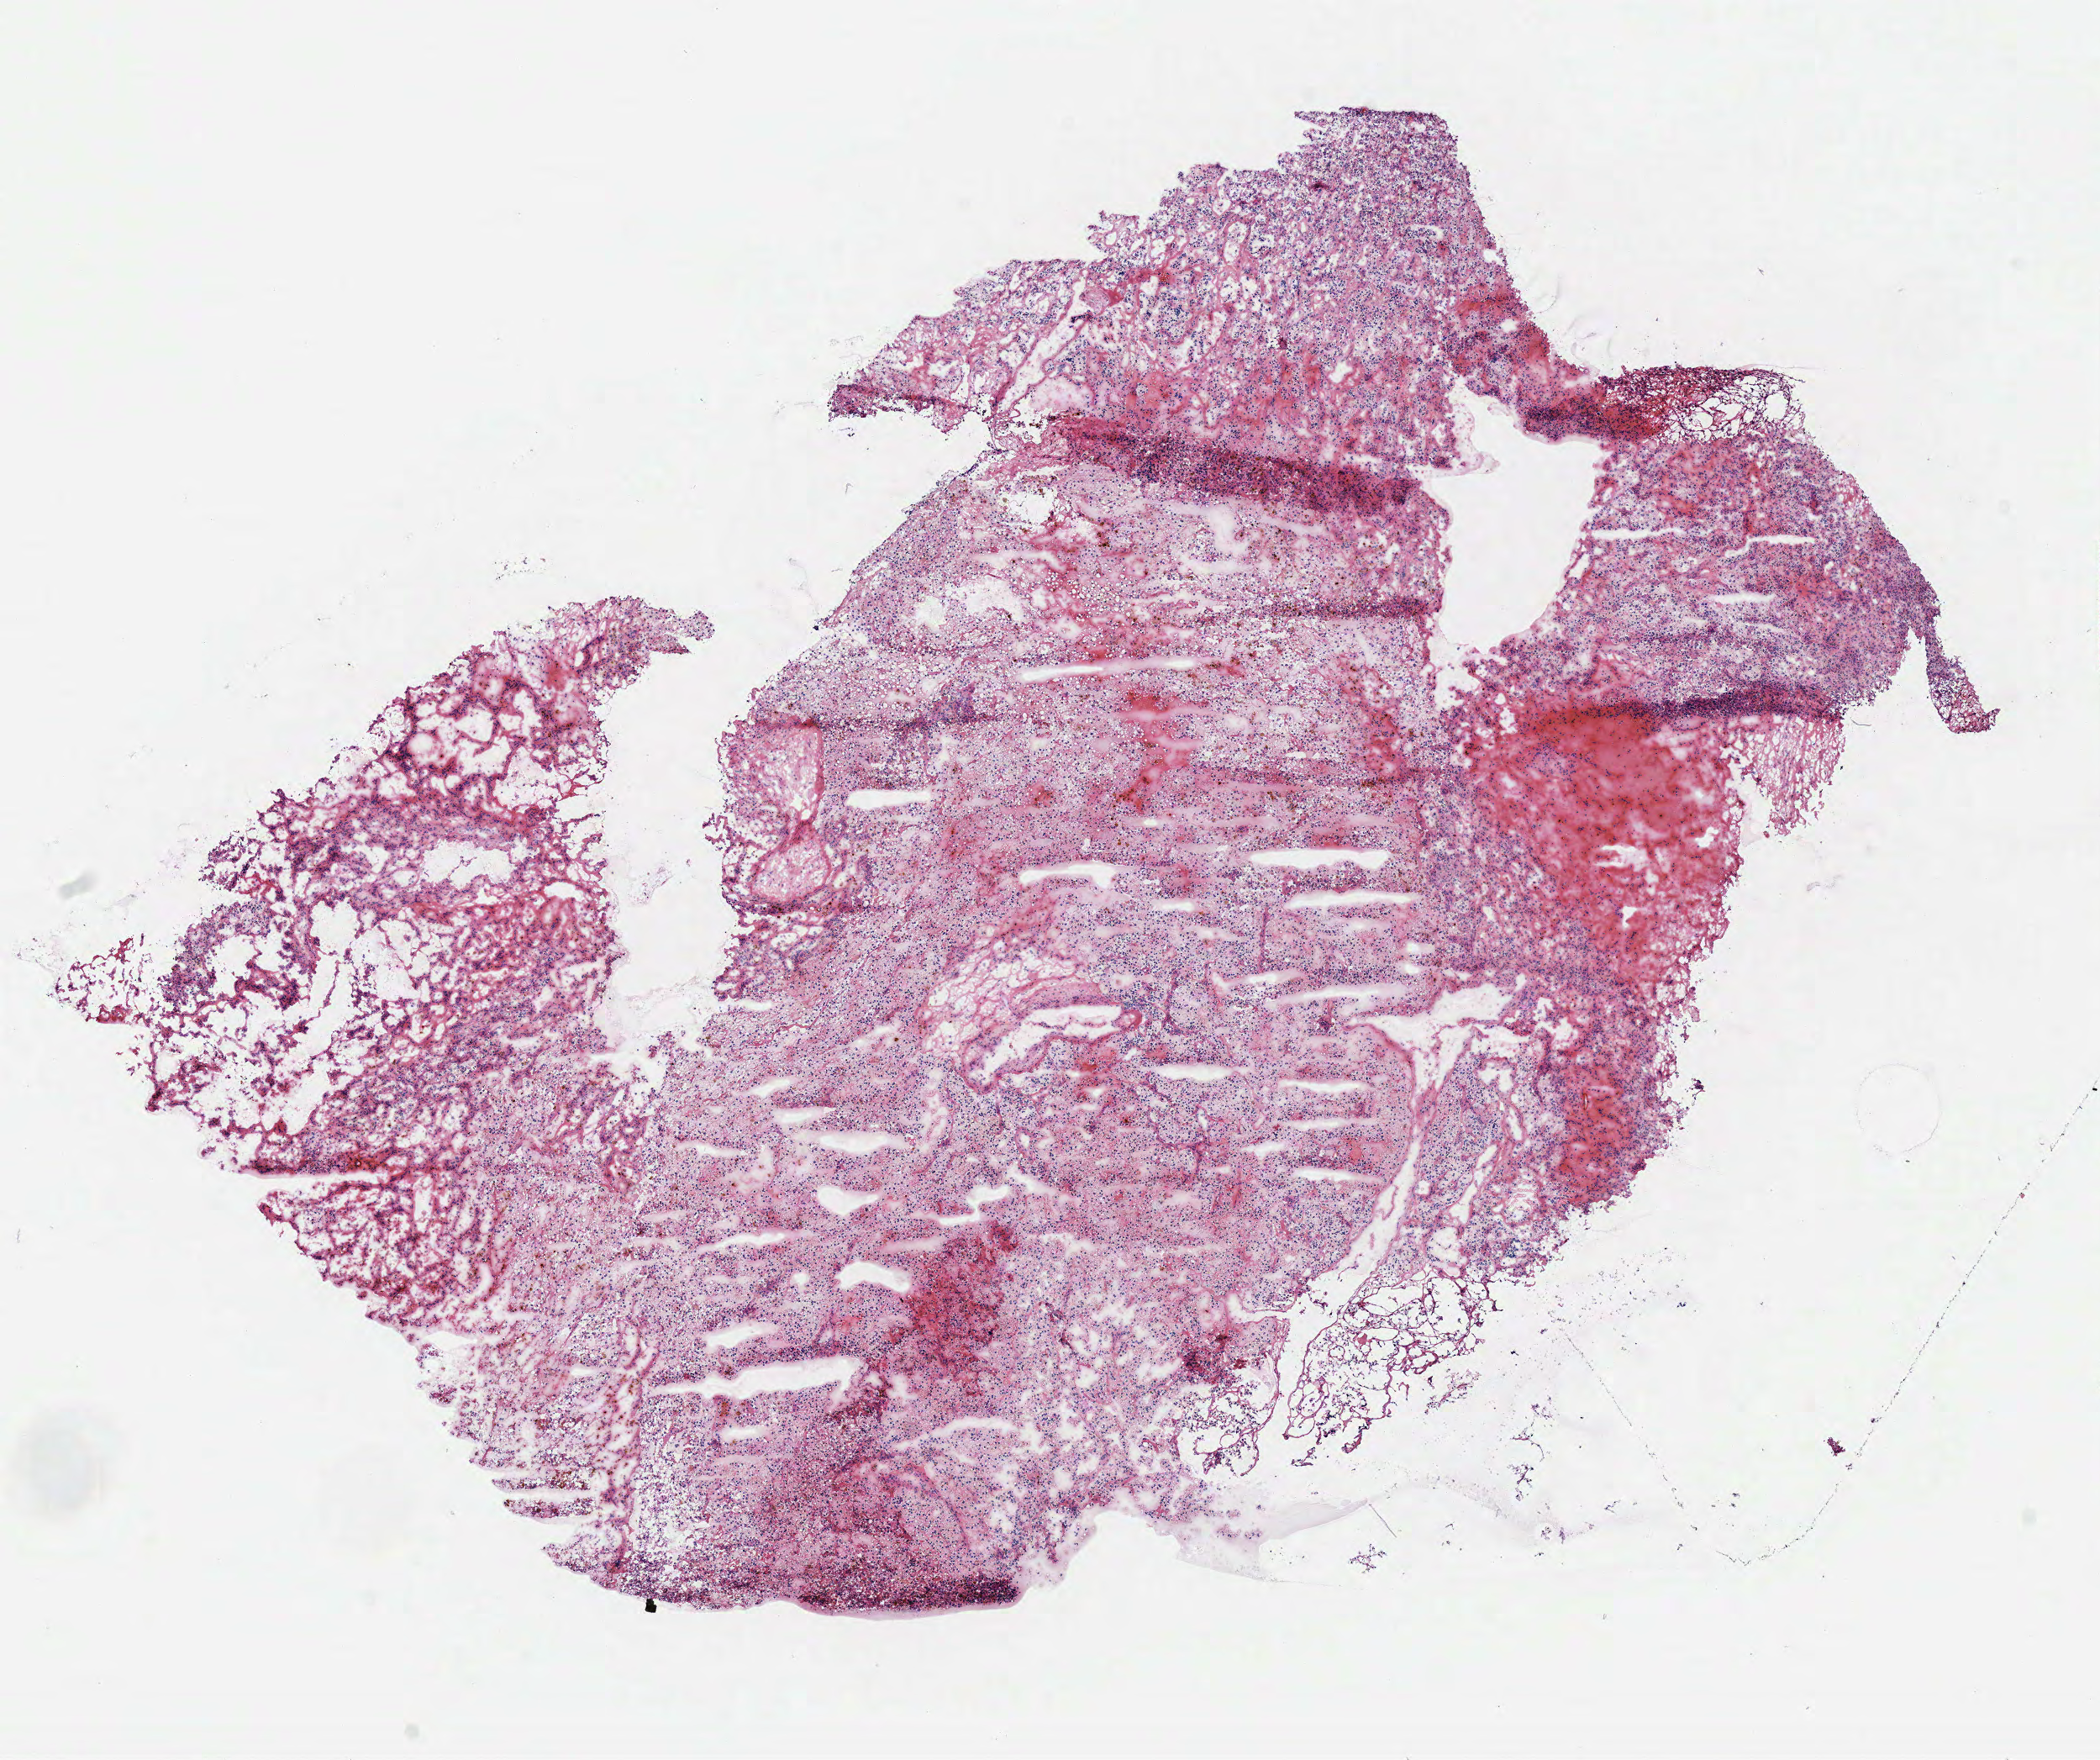
Whole-slide histology image, H&E, whole scanned area (about 9.8 x 8.2 mm) shown as a low-resolution overview, frozen section from the top of the tissue portion, primary tumour sample from the kidney. Patient: male, age at initial diagnosis 68 years. Histologic grade: G3 (poorly differentiated). Slide review estimates, as recorded: tumour cells 90%, tumour nuclei 85%, normal cells 0%, stromal cells 10%, necrosis 0%.
AJCC pathologic stage: I. Histologic diagnosis: Clear cell adenocarcinoma, NOS.